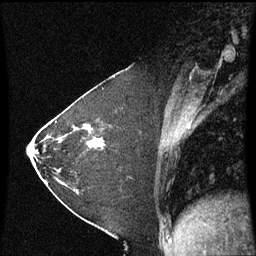
Breast MRI (dynamic contrast-enhanced), one sagittal slice. Position 31 of 60 along the scan axis. Dynamic contrast-enhanced series, image 2 of 3 at this slice position (ordered by acquisition). 1.5 T. TE 4.2 ms, TR 8.9 ms. 256 × 256 image matrix, field of view 200 × 200 mm. Female patient, age 37 years. Case-level facts recorded for this patient, not image findings: setting: breast cancer imaged before/during neoadjuvant chemotherapy; receptor status: HR-positive, HER2-negative.
Structures marked on this image (semi-automatic segmentation, software-assisted and operator-edited):
- analysis volume of interest (the breast-tissue region the enhancement analysis was run in; not a lesion): bounding box (x1, y1, x2, y2) in pixels: (60, 102, 122, 181)
- tumour enhancement mask (voxels above the 70 % enhancement threshold inside the analysis volume of interest): (89, 126, 100, 149)